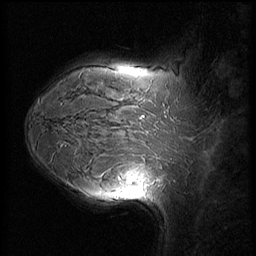
Breast MRI (dynamic contrast-enhanced), one sagittal slice; position 45 of 60 along the scan axis; dynamic contrast-enhanced series, image 2 of 3 at this slice position (ordered by acquisition); 1.5 T; TE 4.2 ms, TR 8.9 ms; 2.5 mm slice thickness; 256 × 256 image matrix, field of view 220 × 220 mm. Female patient, age 37 years. Case-level facts recorded for this patient, not image findings: setting: breast cancer imaged before/during neoadjuvant chemotherapy; receptor status: triple-negative.
Structures marked on this image (semi-automatic segmentation, software-assisted and operator-edited):
- analysis volume of interest (the breast-tissue region the enhancement analysis was run in; not a lesion): bounding box <114,153,159,206> (left, top, right, bottom; pixels)
- tumour enhancement mask (voxels above the 140 % enhancement threshold inside the analysis volume of interest): <120,172,147,187>